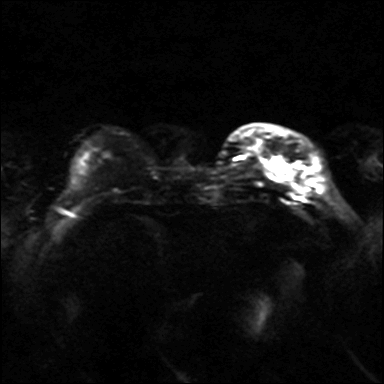
Breast MRI, one axial slice. Position 6 of 36 along the scan axis. Diffusion-weighted series; image 2 of 4 stored at this slice position (different b-values; order by instance number). 3 T. 4 mm slice thickness. 384 × 384 image matrix, field of view 320 × 320 mm. Female patient.
Annotated regions visible in this slice (expert manual segmentation):
- tumour on diffusion-weighted imaging: bounding box [x1, y1, x2, y2] px = [268, 159, 286, 178]